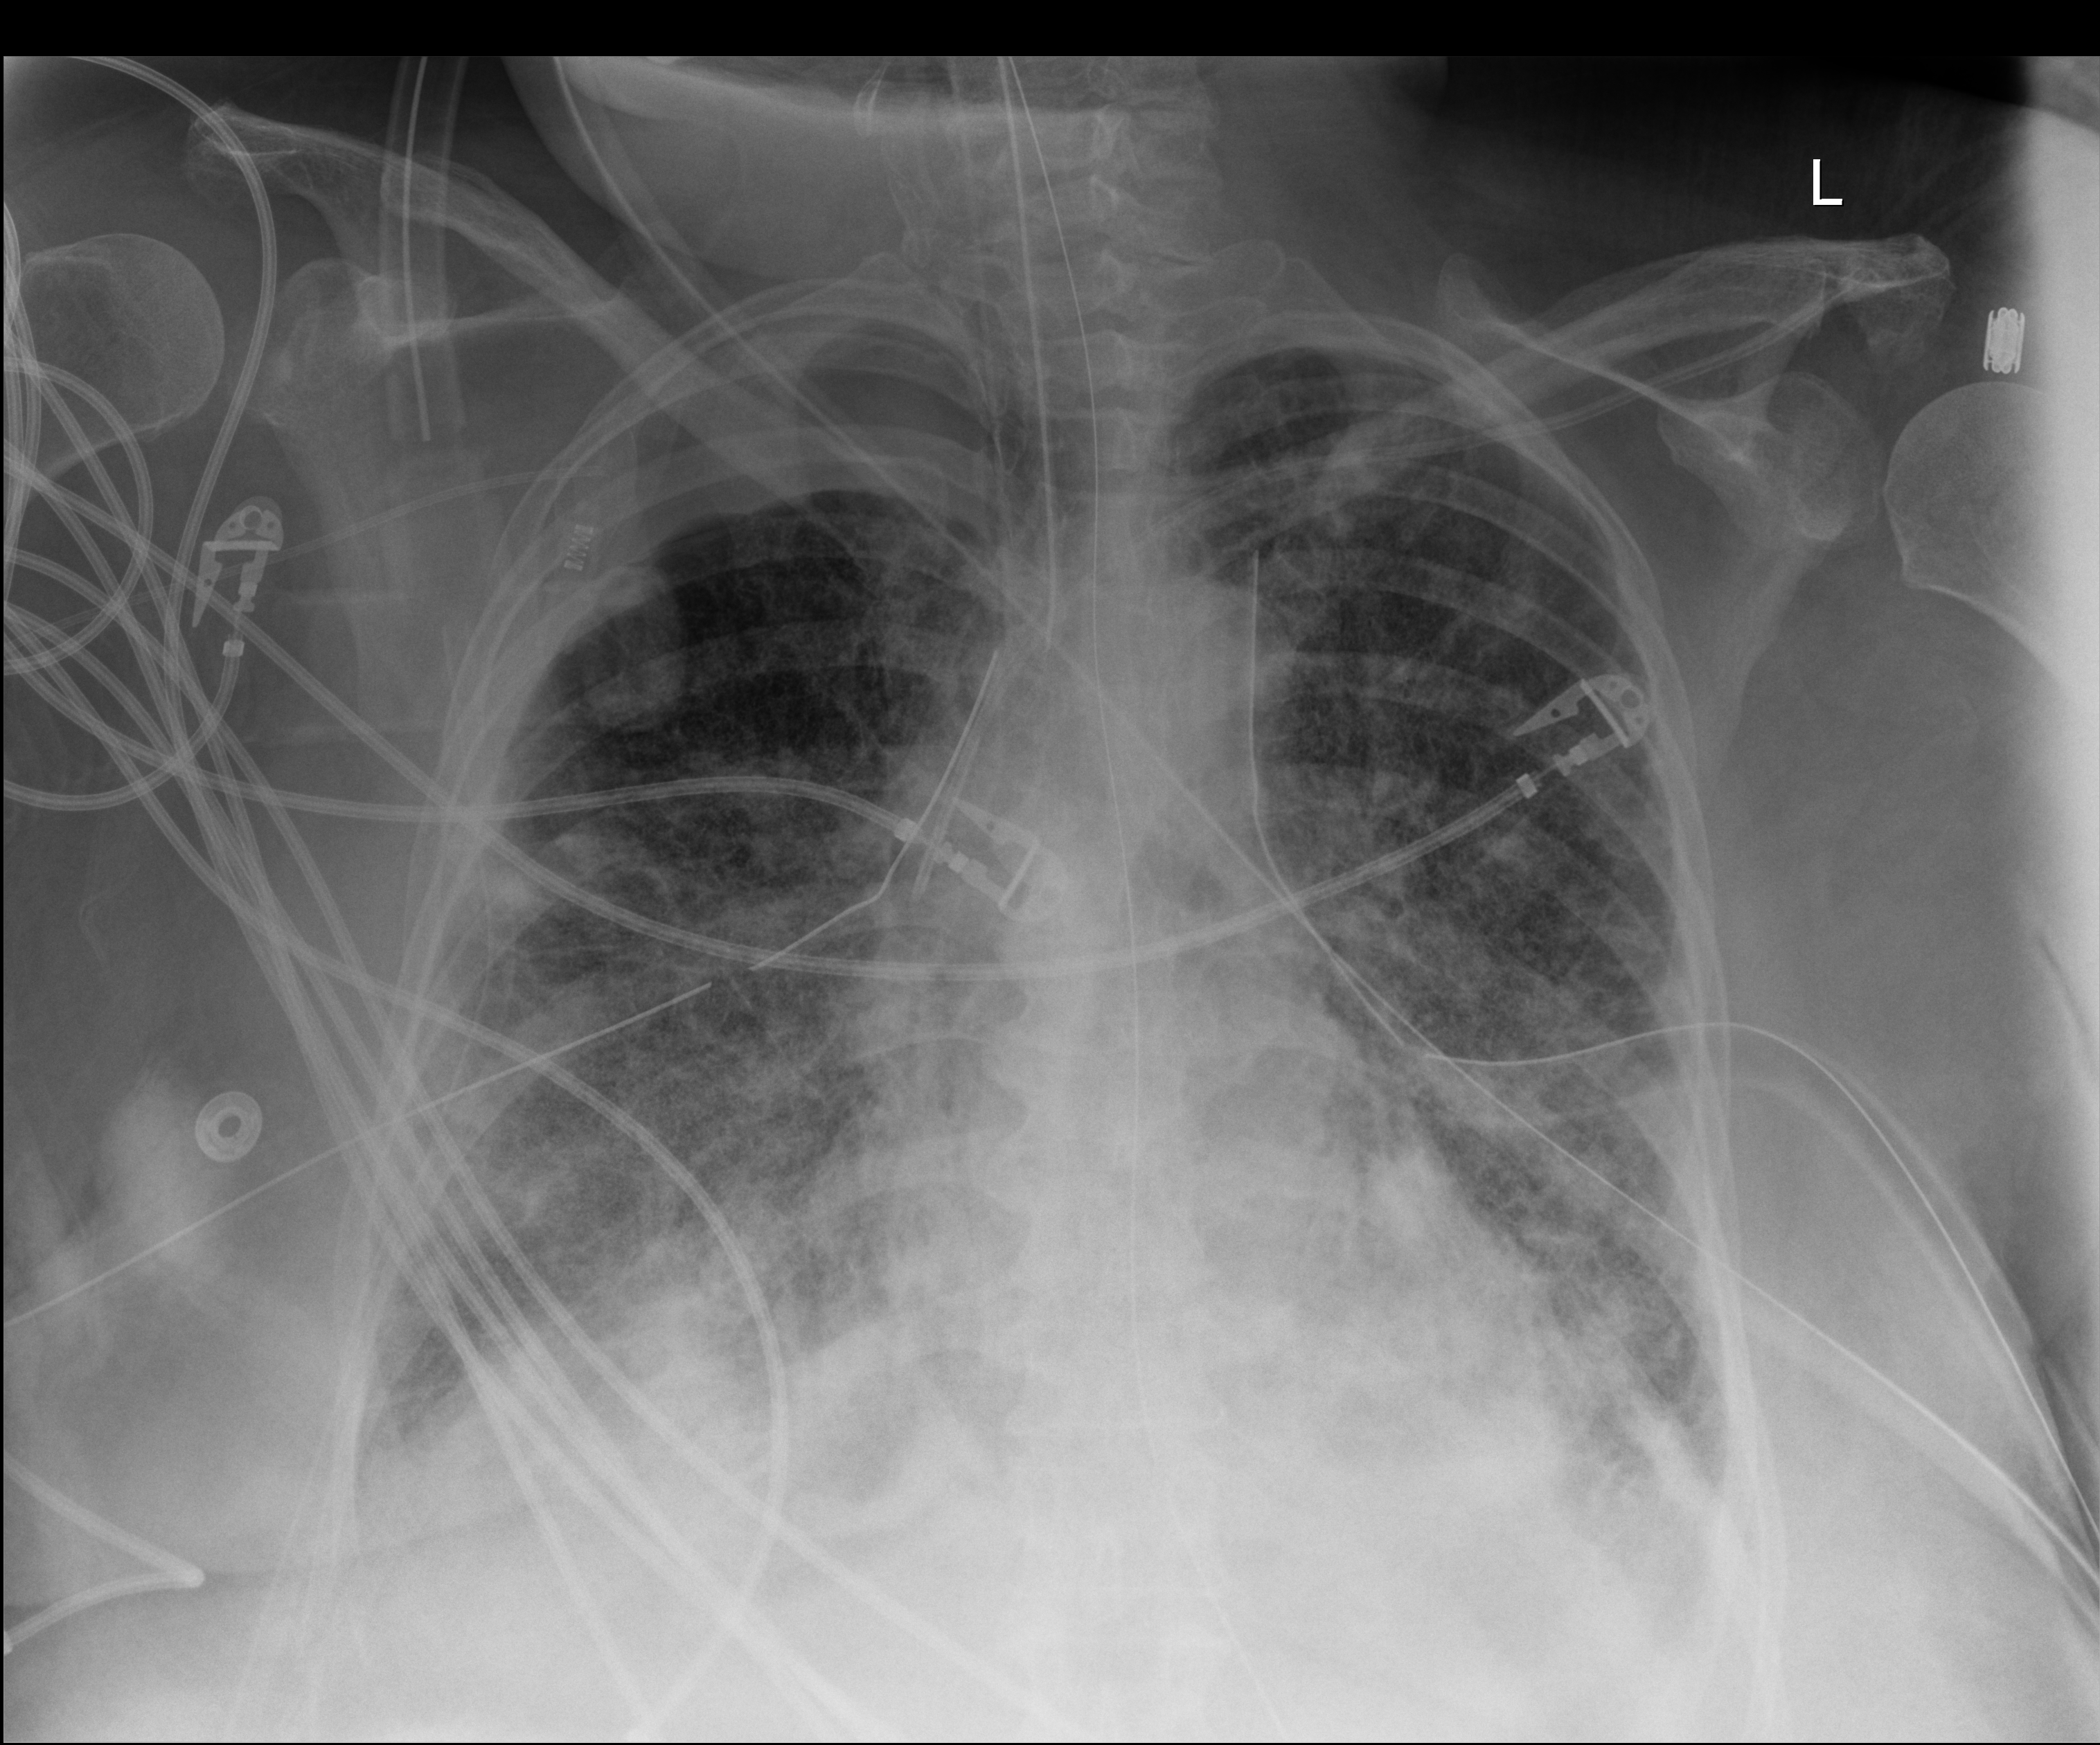
Chest X-ray (portable); anteroposterior (AP) projection. Female patient hospitalised with COVID-19, age 60–74 years.
Hospital-stay facts (about this admission, not read from this image; timing relative to this image not recorded): admitted to intensive care during this hospital stay: yes; chronic kidney disease (admission record): no.